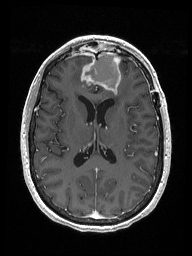
Brain MRI from a brain-tumour surgery series, one axial slice; T1-weighted post-contrast; 1 mm slice thickness; 192 × 256 image matrix, field of view 187 × 250 mm. From the clinical record (not read from this slice): histopathology: Metastastic Carcinoma from Breast primary; tumour location: Right Frontal.
Annotated regions visible in this slice (outlined manually by an expert reader):
- previous resection cavity: bounding box [x1, y1, x2, y2] px = [86, 53, 121, 93]